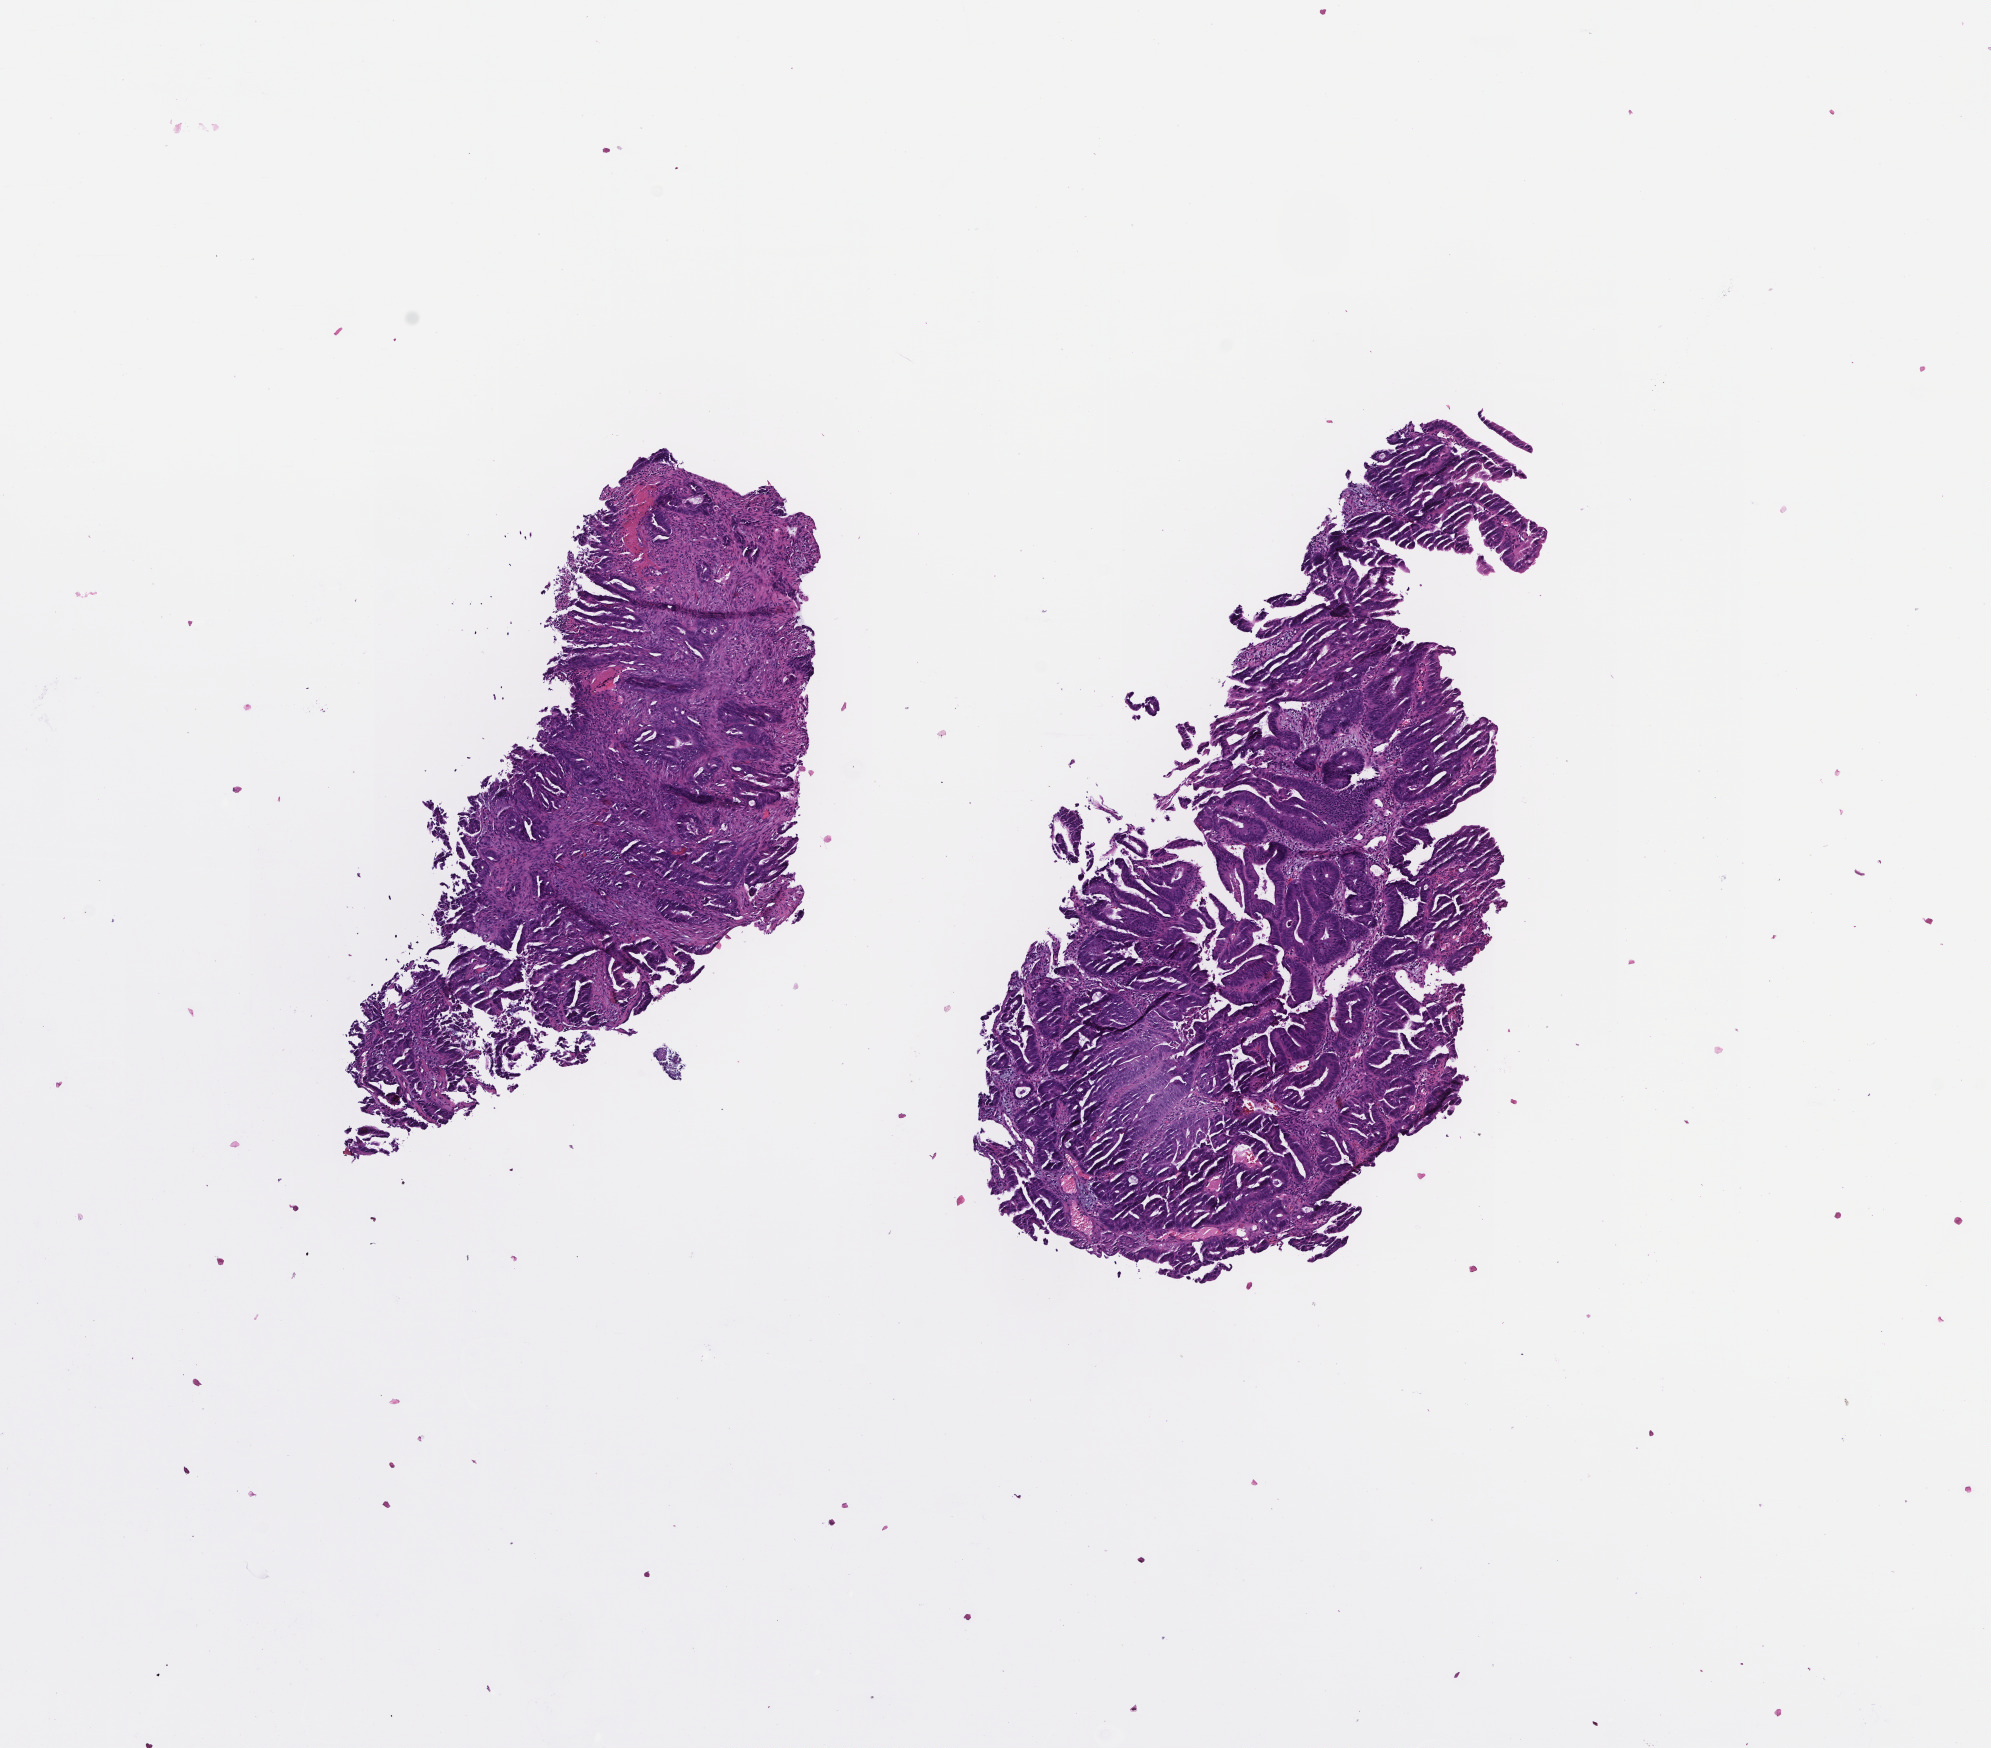
Digitized hematoxylin and eosin (H&E)-stained section — whole scanned area (about 8.0 x 7.1 mm) shown as a low-resolution overview. FFPE section. Site: colon. Specimen time point: archival tissue. Patient: female.
This section: primary tumour tissue. Diagnosis: Colorectal Carcinoma.